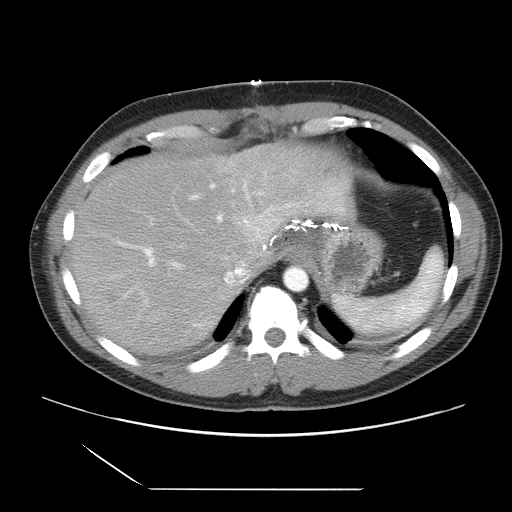
Contrast-enhanced abdominal CT, one axial slice; position 24 of 39 along the scan axis; intravenous contrast given; soft-tissue window (W 400 / L 40 HU); 512 × 512 image matrix, field of view 395 × 395 mm. Male patient, age 39 years. Case-level facts recorded for this patient, not image findings: diagnosis: colorectal cancer liver metastases, imaged before liver resection; multiple liver metastases: yes; largest metastasis: 1.3 cm; disease in both lobes: no.
Outlined on this slice (manually delineated by an expert):
- hepatic veins: bounding box <201,260,249,302> (left, top, right, bottom; pixels)
- liver: <73,146,350,356>
- planned liver remnant (the part of the liver to remain after resection): <121,145,351,266>
- portal vein (with intrahepatic branches): <113,183,257,307>
- liver metastasis: <108,294,118,303>